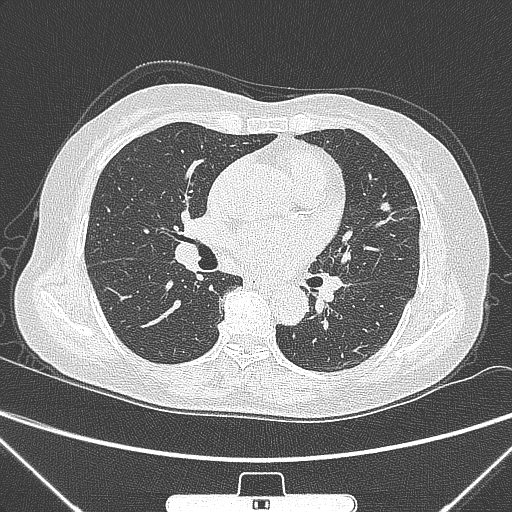
Chest CT, one axial slice; 120 kVp; lung window (W 1500 / L -600 HU); 512 × 512 image matrix. Patient: female, 70 years. From the clinical record (not read from this slice): clinical TNM (as recorded): T1b N0 M0; histopathological grade: G2.
Outlined on this slice (bounding box drawn by a radiologist):
- lung tumour (recorded histology: adenocarcinoma): box from (x=371, y=199) to (x=396, y=215) px